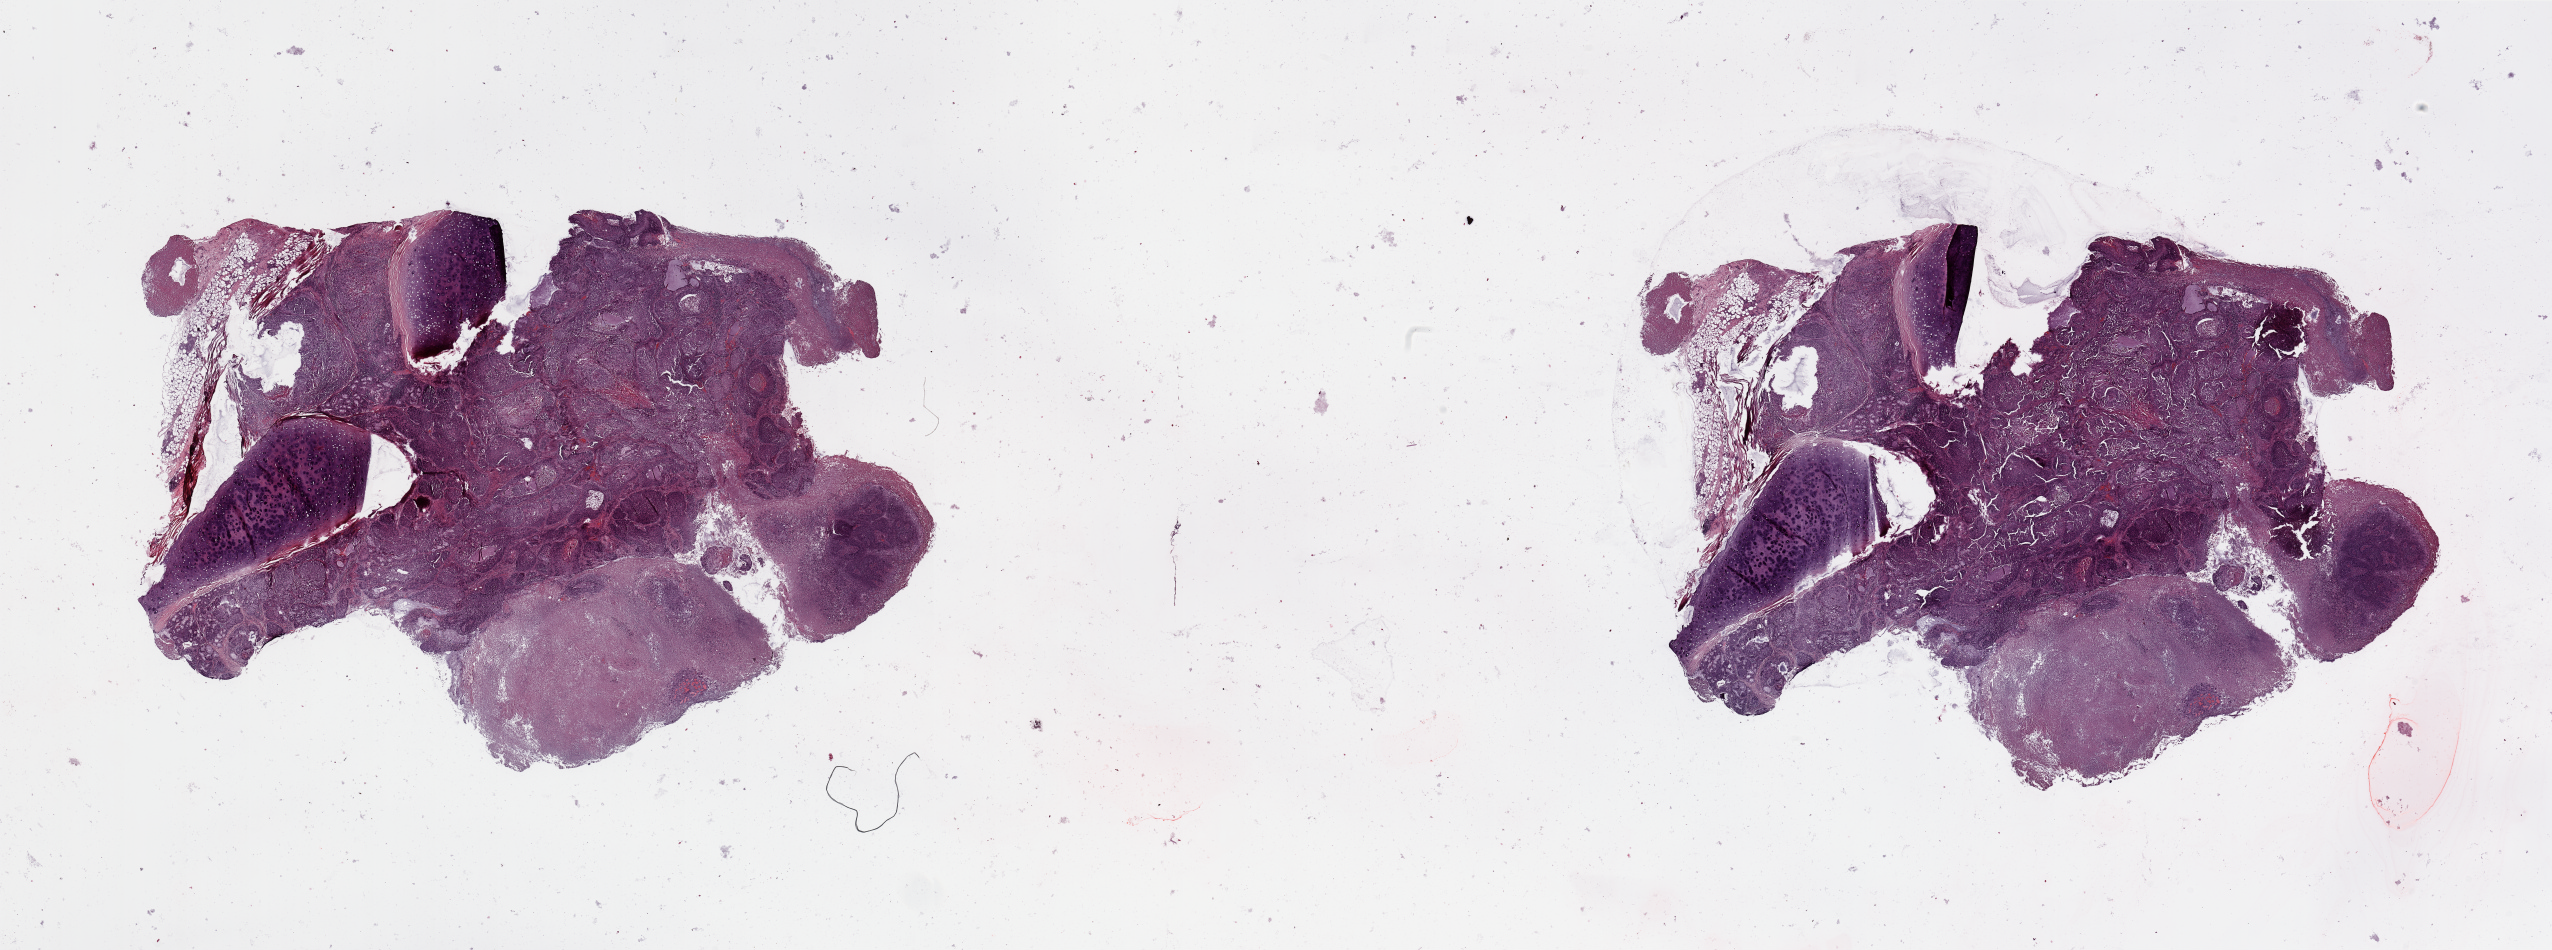
Digitized Hematoxylin and eosin (H&E) stained tissue section (whole slide), whole scanned area (about 40.4 x 15.0 mm) shown as a low-resolution overview; lung, tumour tissue. 66-year-old male patient. Histologic grade: G2 (moderately differentiated).
Histologic diagnosis: Squamous cell carcinoma, NOS. AJCC pathologic stage: IIA. Primary tumour site (as recorded): left upper lobe.